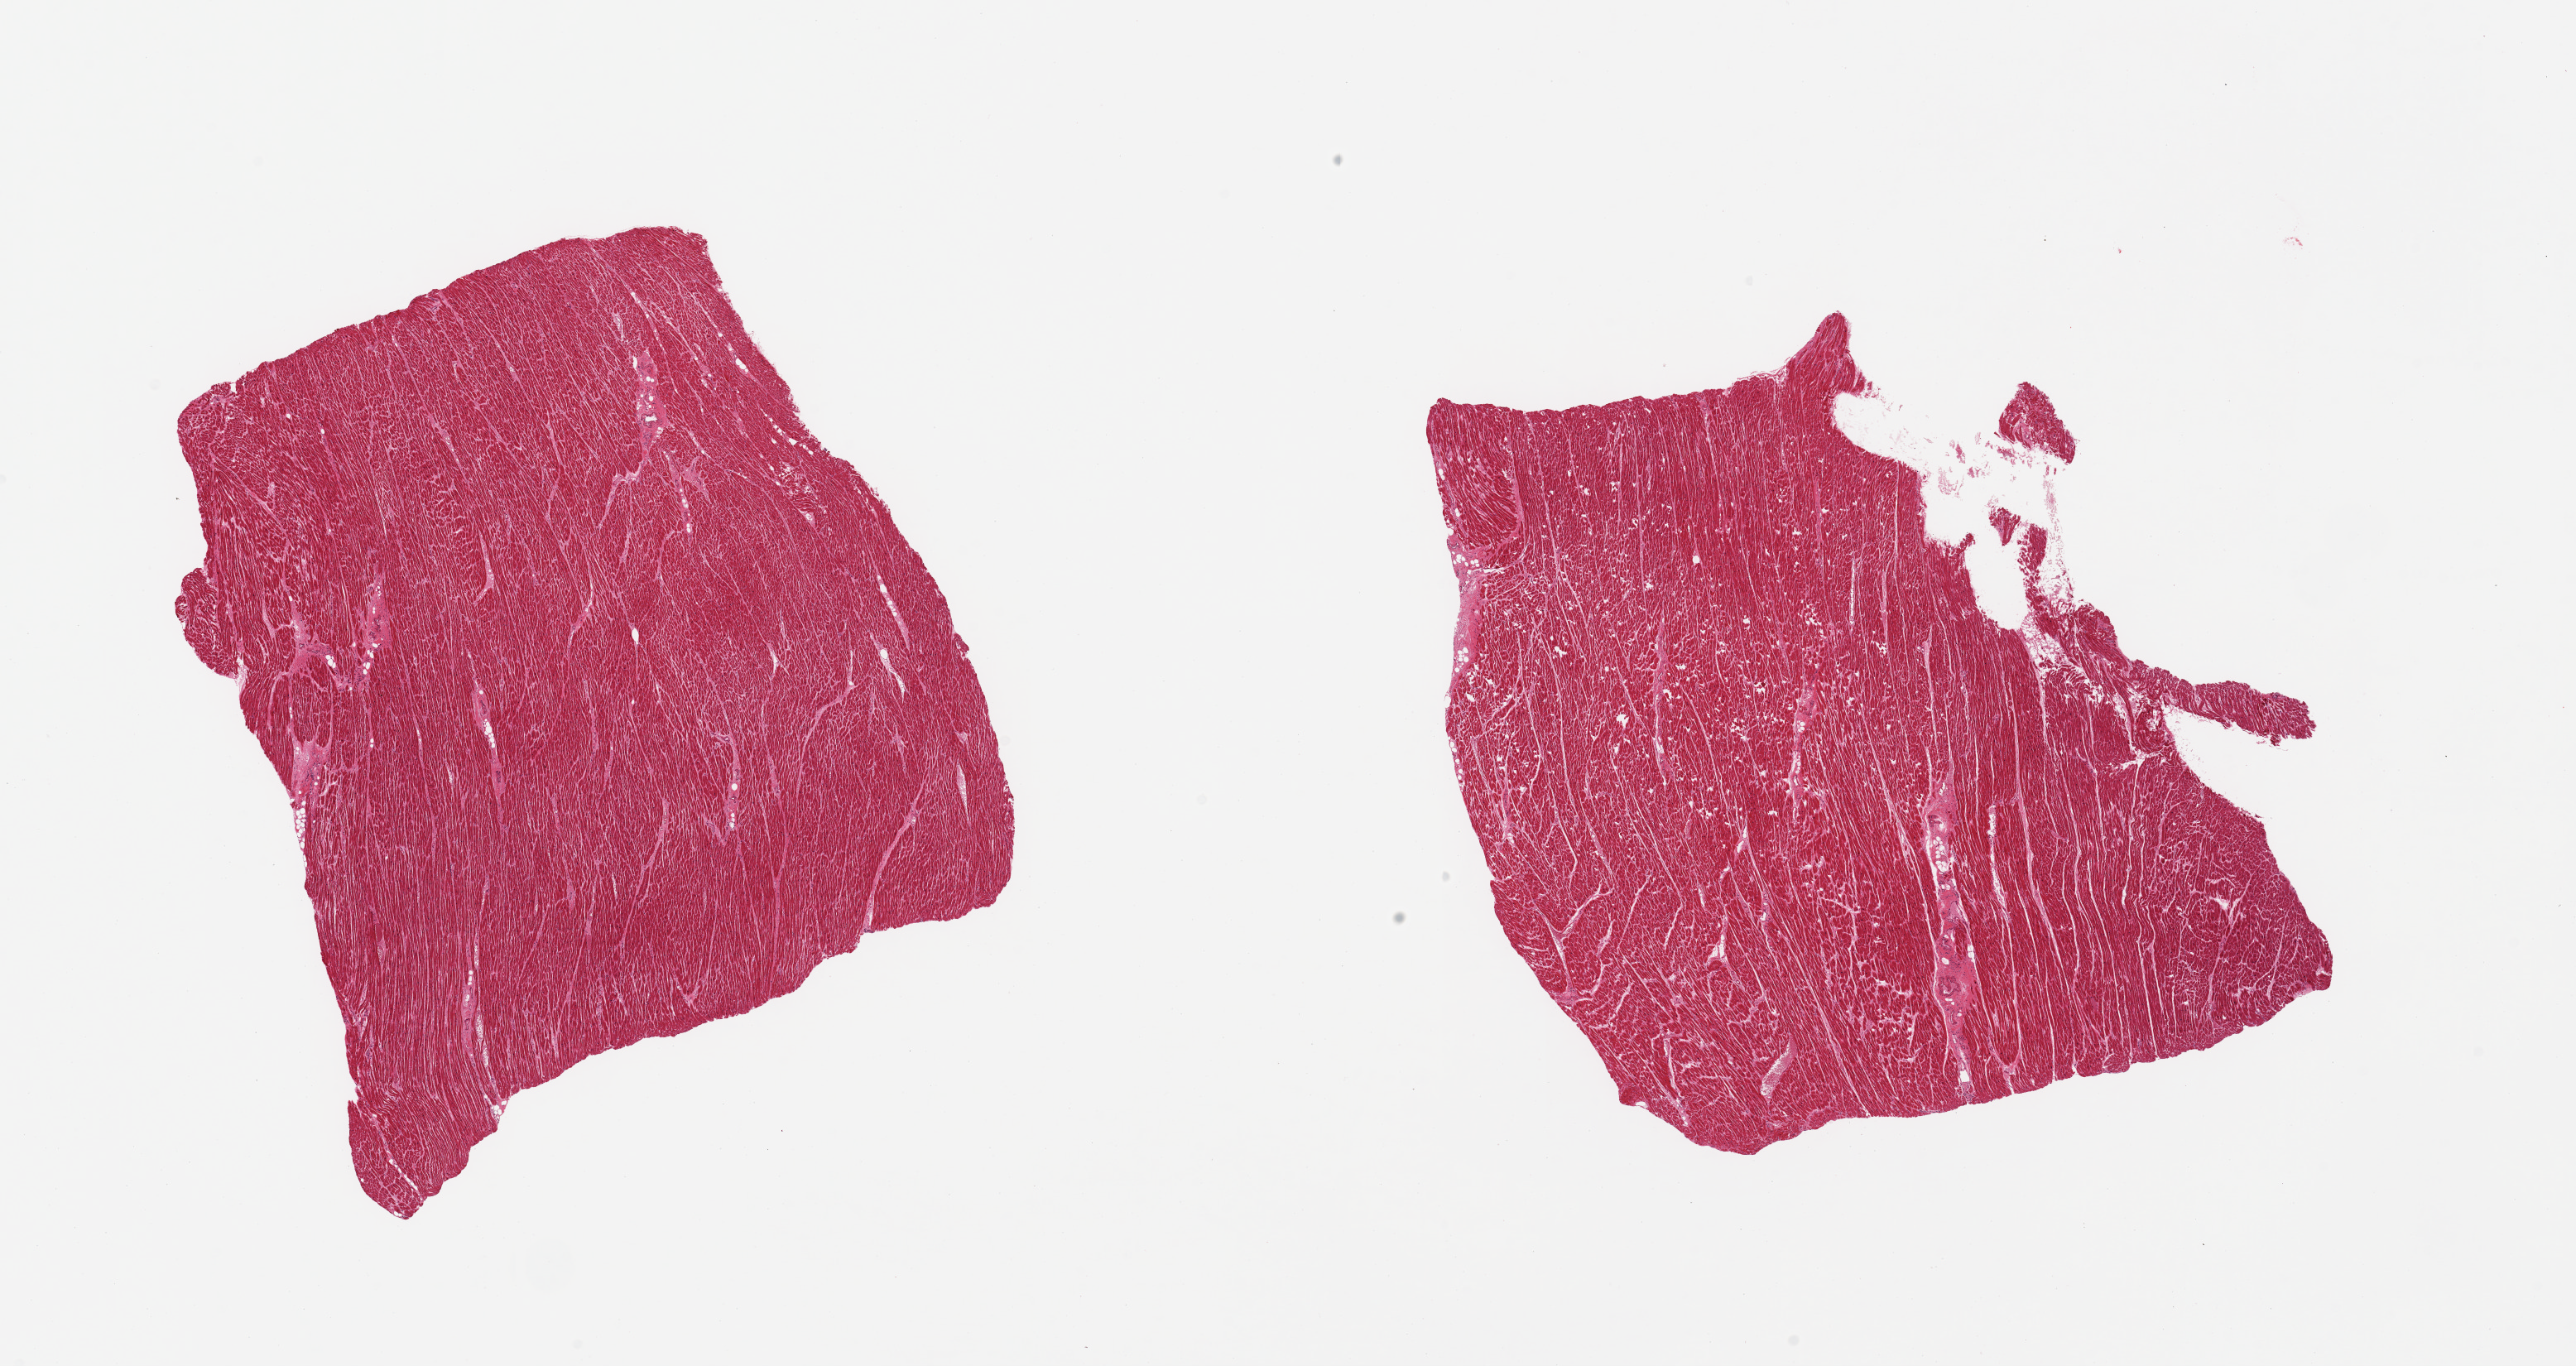
Digitized H&E-stained section, brightfield, a low-resolution overview of the entire scanned area, about 24.6 x 13.0 mm; PAXgene-fixed paraffin-embedded (PFPE) section; sampled site (target tissue): heart; donor tissue sample. Donor sex: male.
Review note (as recorded): 2 pieces; some hypertrophy.